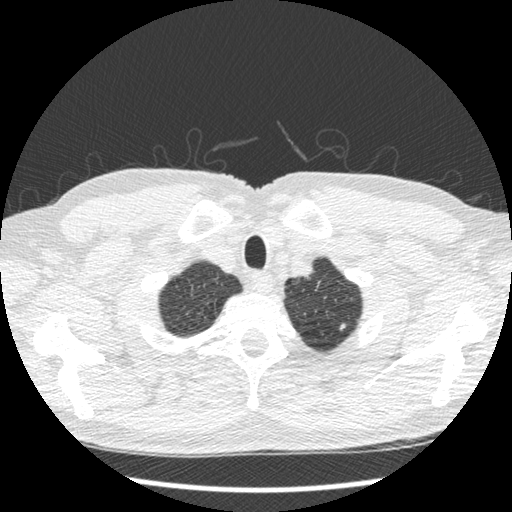
Low-dose screening chest CT, one axial slice. Position 412 of 439 along the scan axis. Reconstruction kernel STANDARD. 120 kVp. Lung window (W 1500 / L -600 HU). 1.25 mm slice thickness. 512 × 512 image matrix.
Annotated regions visible in this slice (outlined manually by an expert reader):
- lesion 1 (nodule, upper lobe of left lung): box from (x=340, y=323) to (x=346, y=330) px